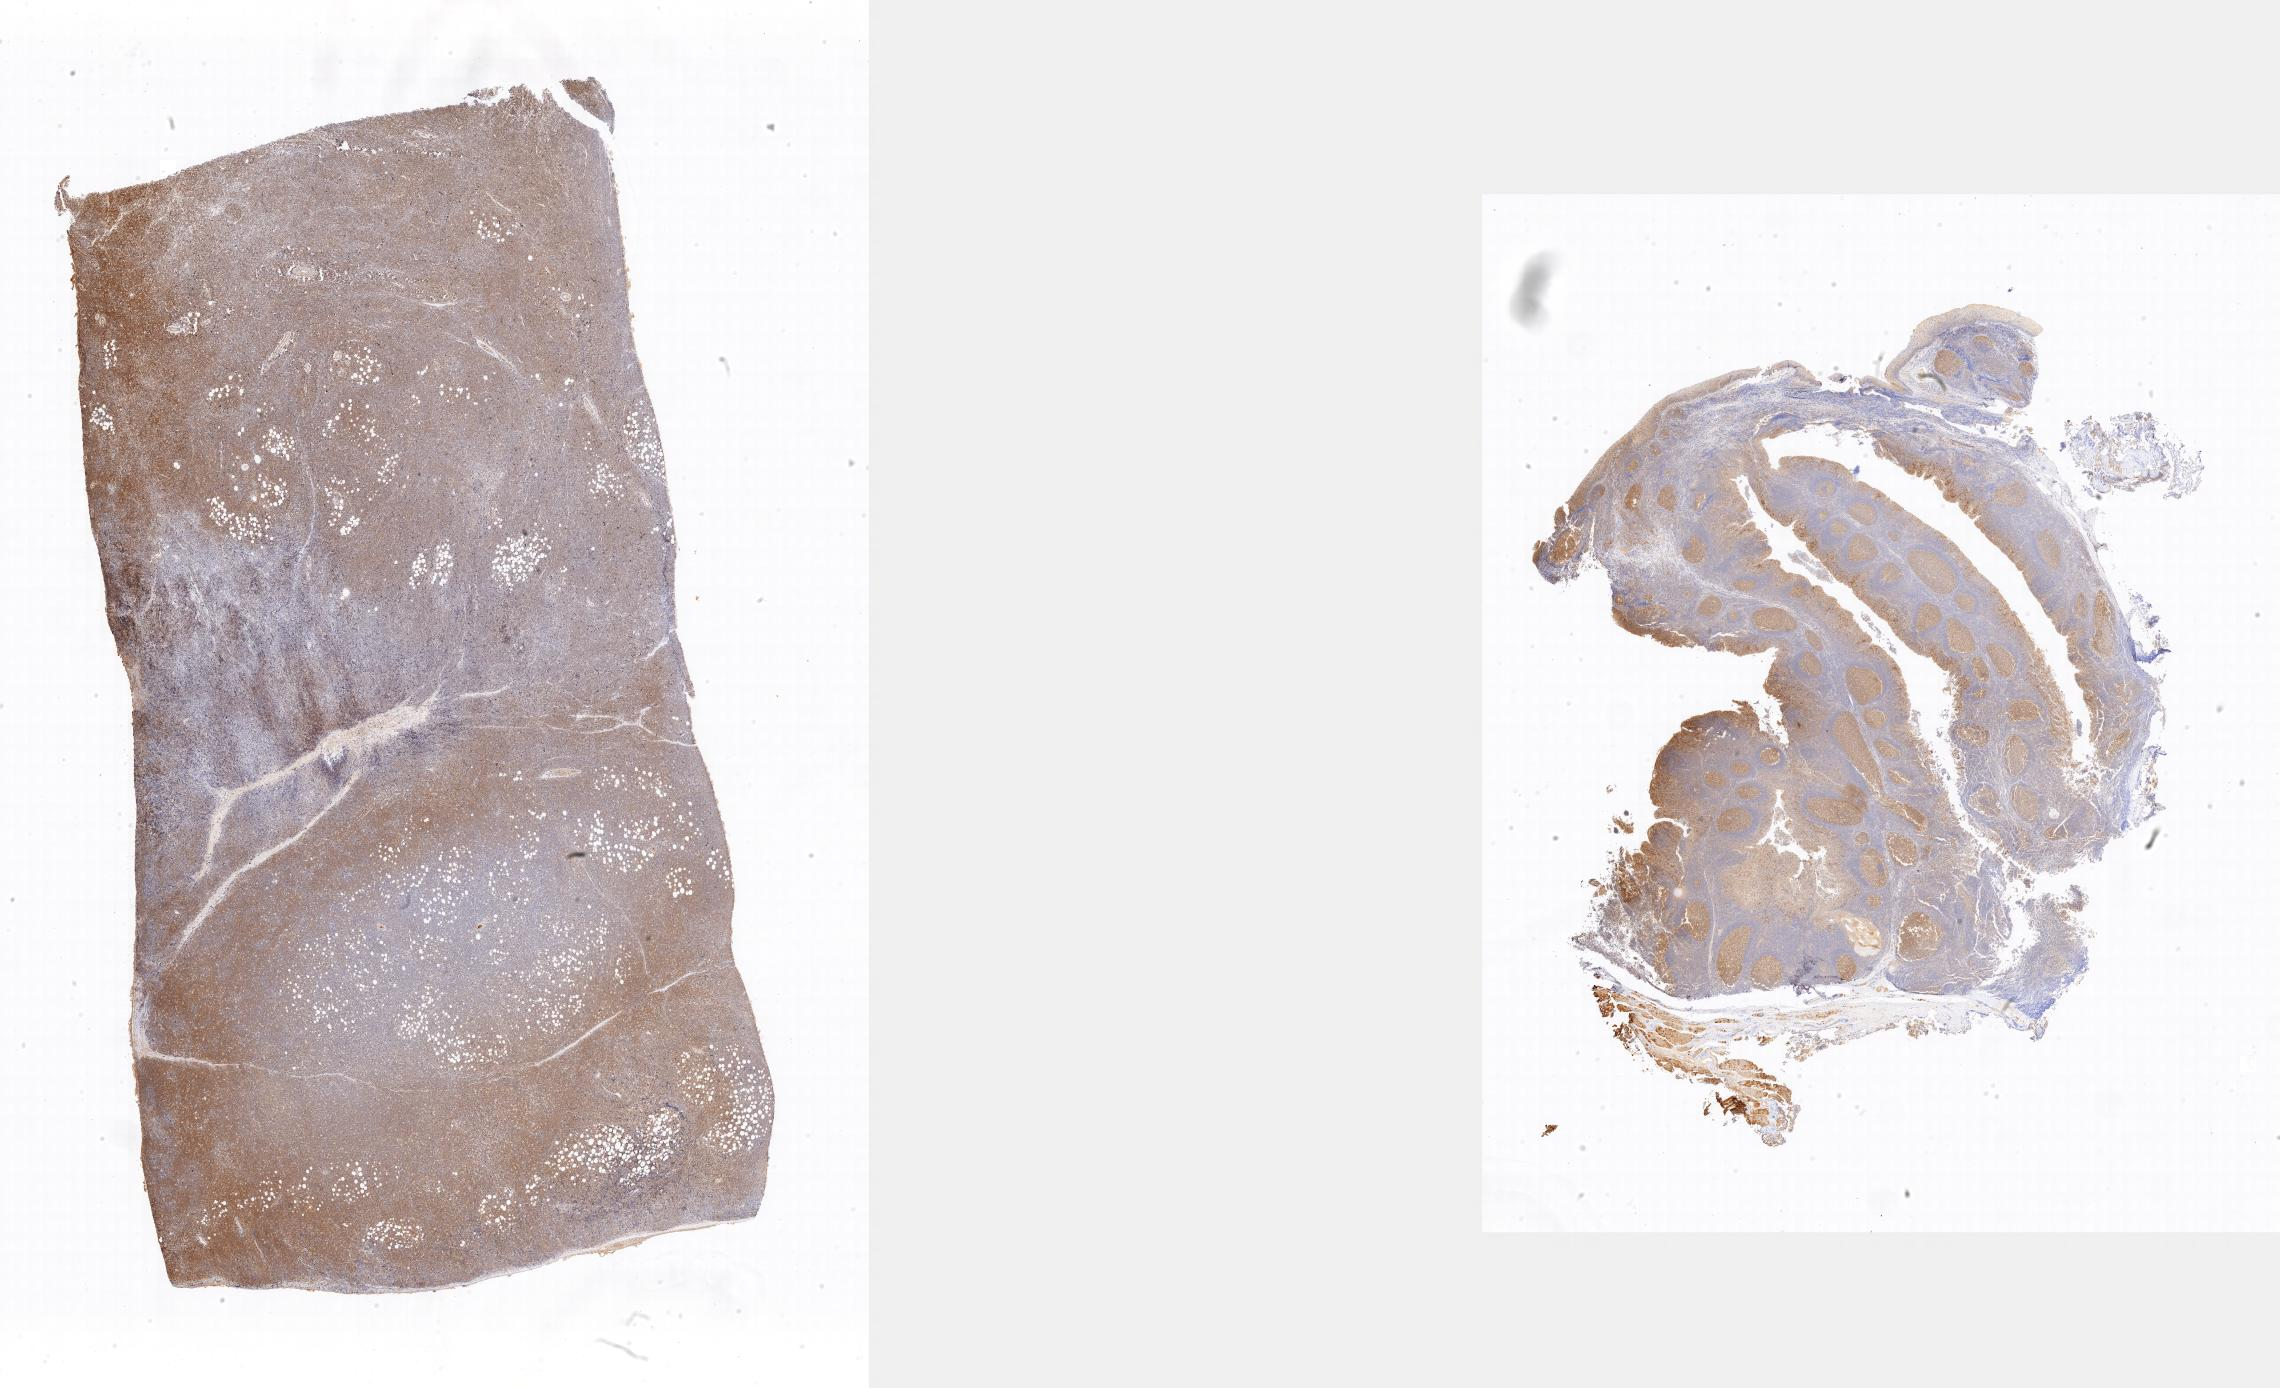
IHC for BCL6, whole-slide image — low-resolution overview of the scanned area; tumor tissue; site: colon. Patient: female, age 12 years.
Diagnosis: Burkitt lymphoma, NOS.